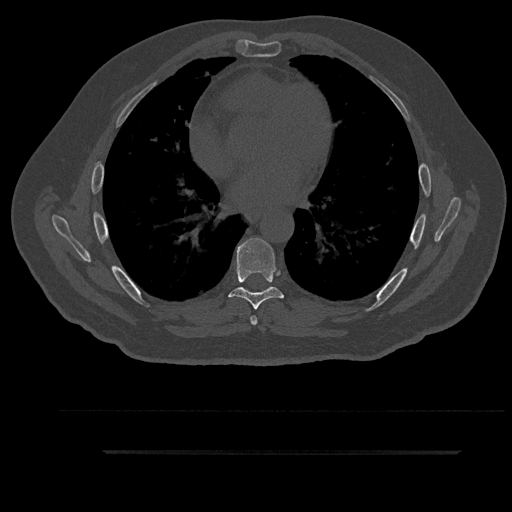
CT including the spine, one axial slice. Position 530 of 797 along the scan axis. Reconstruction kernel Br40s/3. 120 kVp. Bone window (W 1800 / L 400 HU). 0.5 mm slice thickness. 512 × 512 image matrix, field of view 432 × 432 mm. Male patient, age 63 years. From the clinical record (not read from this slice): primary cancer: renal.
Structures marked on this image (semi-automatically segmented with operator editing):
- T6 vertebra: box from (x=250, y=292) to (x=262, y=325) px
- T7 vertebra: (x=228, y=238)–(x=284, y=310)